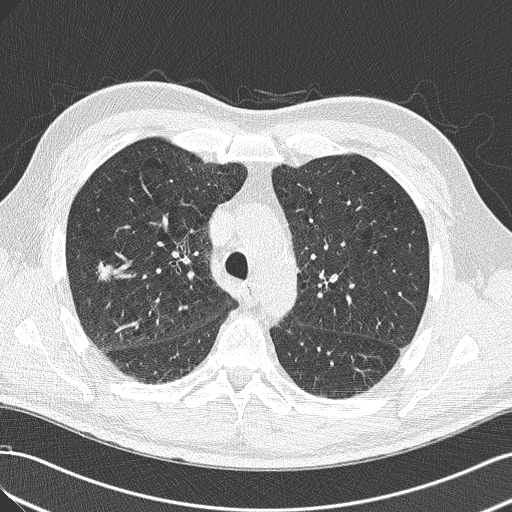
Low-dose screening chest CT, one axial slice. Position 95 of 143 along the scan axis. Reconstruction kernel B50f. 120 kVp. Lung window (W 1500 / L -600 HU). 2 mm slice thickness. 512 × 512 image matrix, field of view 360 × 360 mm.
Outlined on this slice (expert manual segmentation):
- lesion 1 (tumor, lower lobe of right lung): box from (x=98, y=262) to (x=114, y=281) px